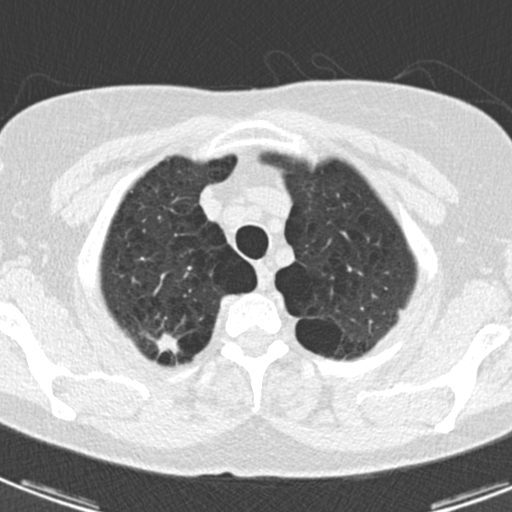
Low-dose screening chest CT, one axial slice; position 154 of 174 along the scan axis; reconstruction kernel B30f; 120 kVp; lung window (W 1500 / L -600 HU); 2 mm slice thickness; 512 × 512 image matrix.
Structures marked on this image (expert manual segmentation):
- lesion 1 (tumor, upper lobe of right lung): bounding box [x1, y1, x2, y2] px = [156, 332, 178, 353]